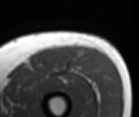
MRI of an extremity soft-tissue mass, one axial slice; position 36 of 86 along the scan axis; MR volume resampled by the dataset authors to the PET/CT grid (not the native acquisition matrix); 3.27 mm slice thickness; 139 × 117 image matrix, field of view 136 × 114 mm. Male patient. Case-level facts recorded for this patient, not image findings: histological type: extraskeletal osteosarcoma; grade: high; site of the primary tumour: thigh.
Outlined on this slice (expert contour drawn on MRI and transferred to this co-registered scan by the dataset authors):
- gross tumour volume (mass): bounding box [x1, y1, x2, y2] px = [68, 50, 82, 74]